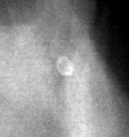
Cropped region of a digitized screen-film mammogram centred on a radiologist-marked abnormality, left breast, CC view.
- Finding: calcifications, morphology lucent center / punctate; BI-RADS assessment category 2; benign without callback (not worked up further).